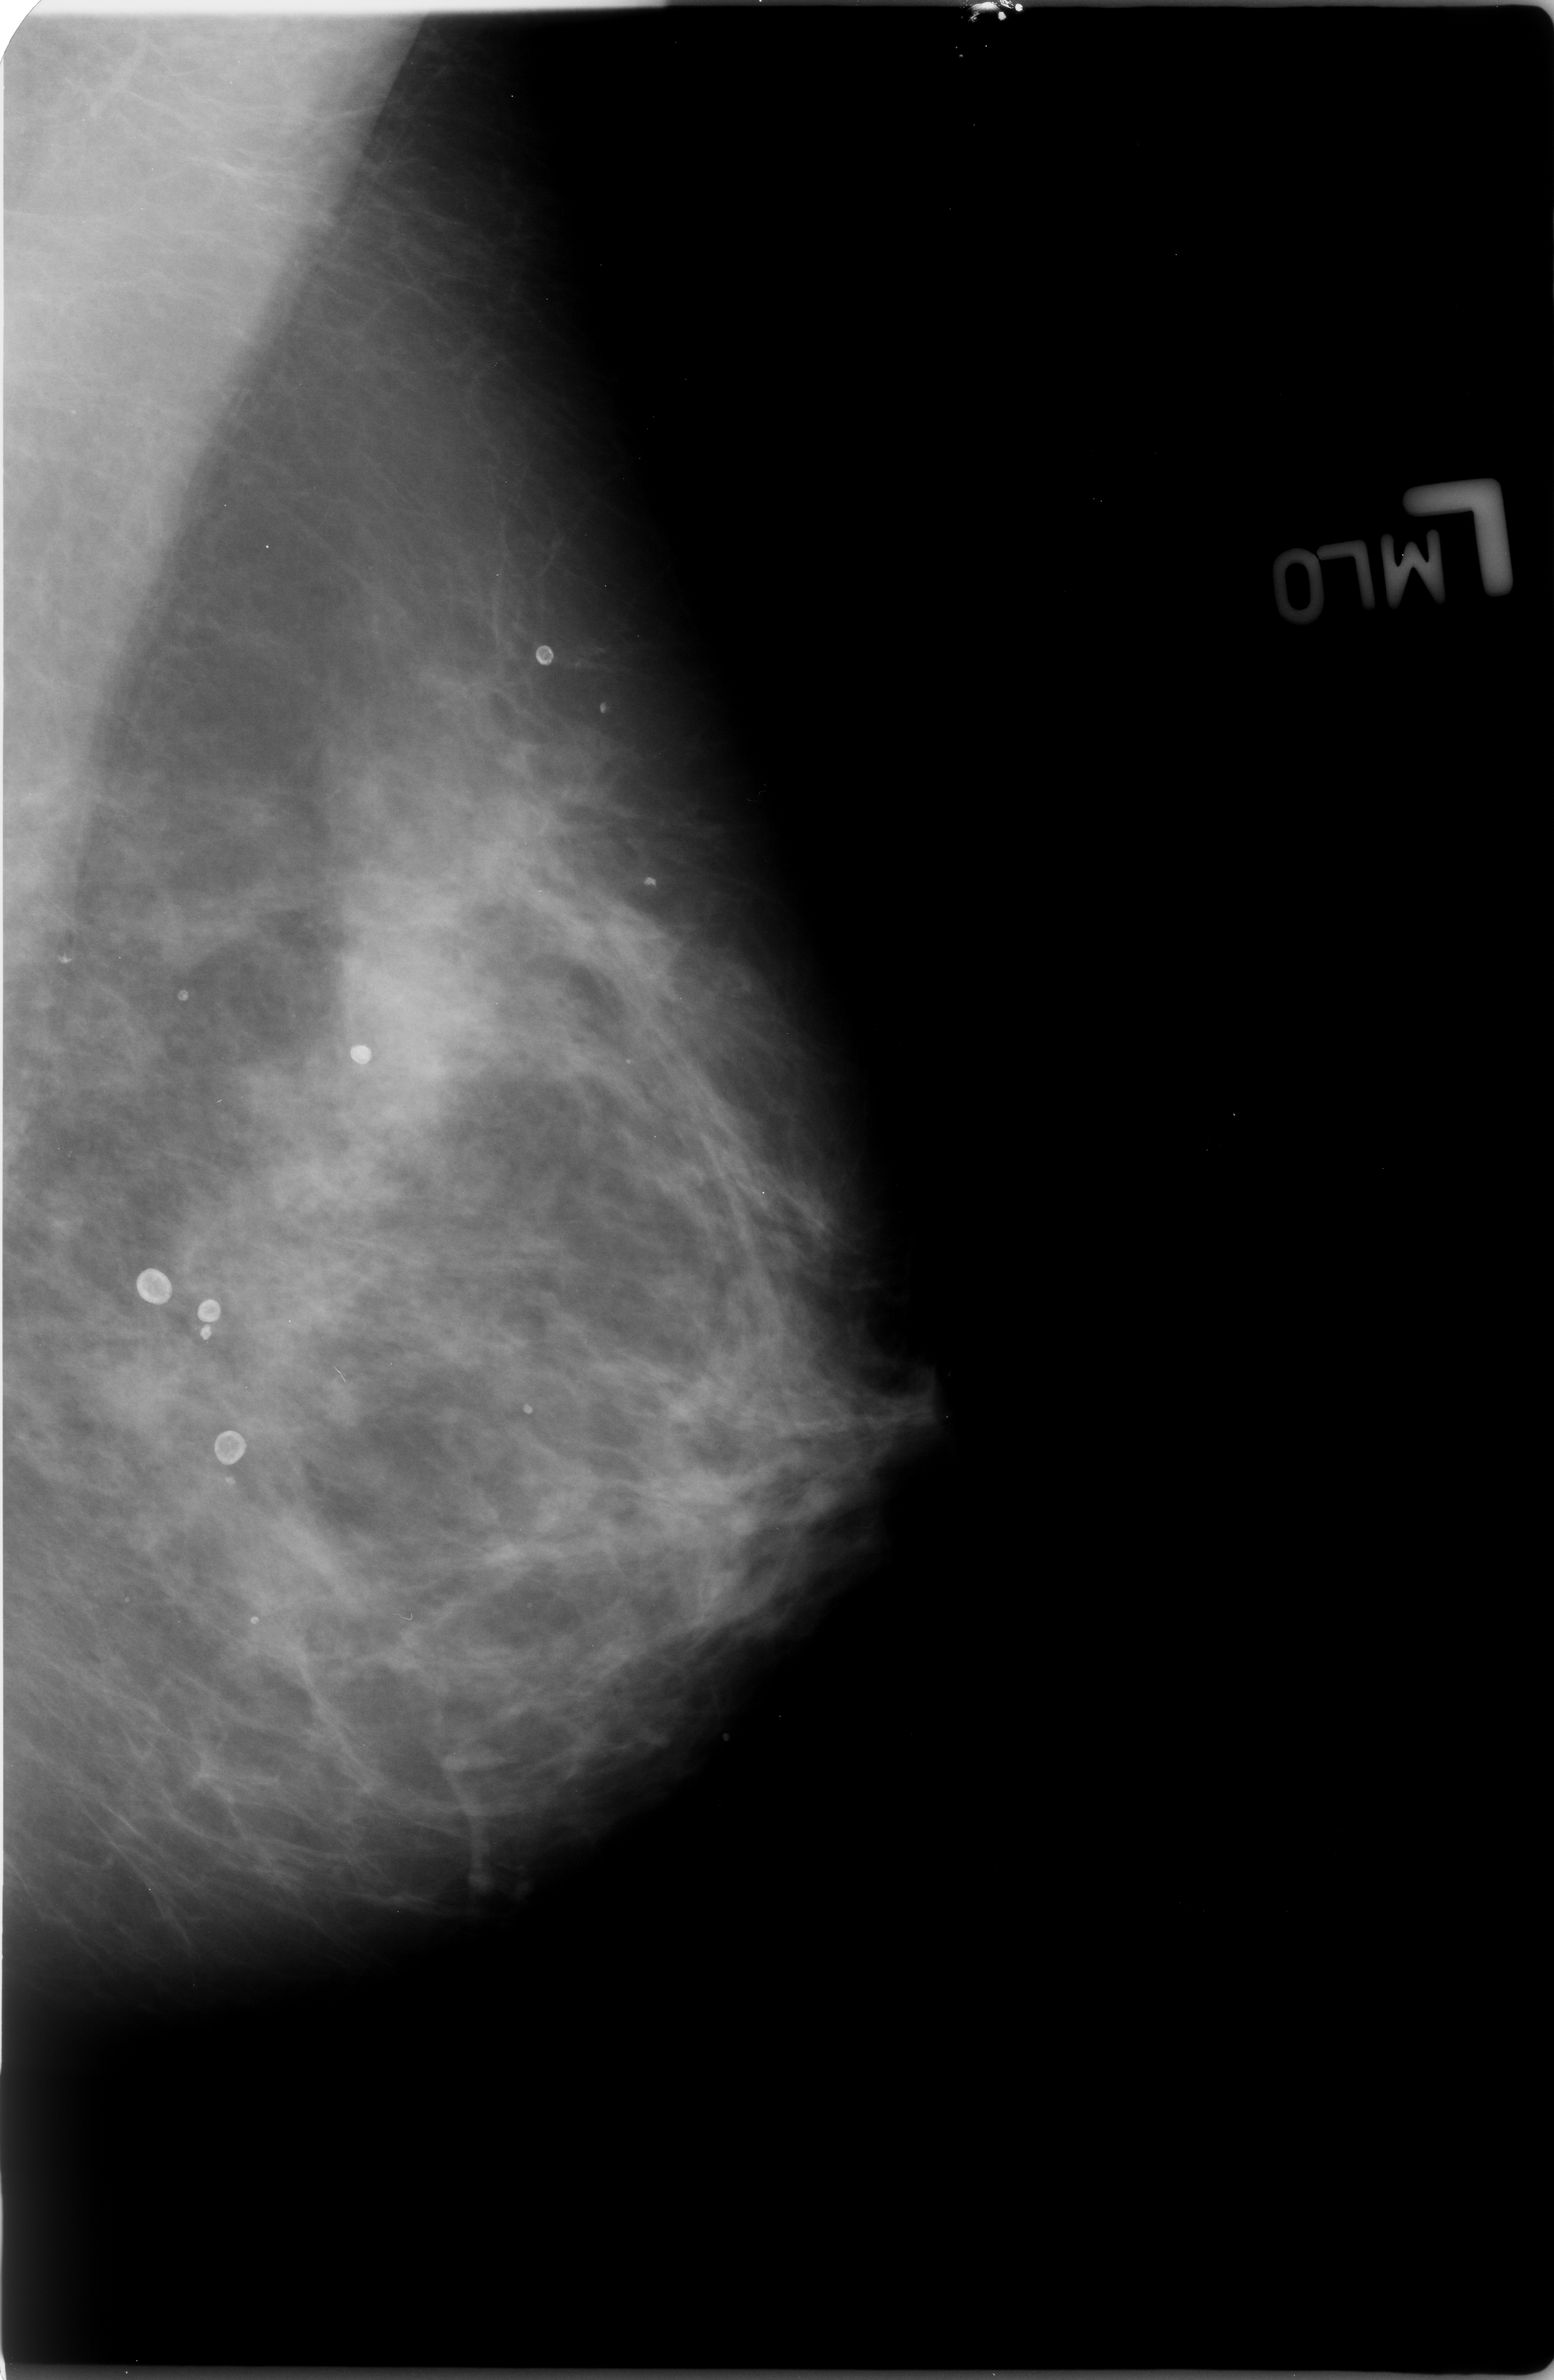
Mammogram (digitized film), left breast, mediolateral oblique (MLO) view, BI-RADS breast density category 3 (scale 1–4).
Abnormality record for this image: Finding 1 of 6: calcifications, morphology round and regular / eggshell; BI-RADS assessment category 2; benign without callback (not worked up further). Finding 2 of 6: calcifications, morphology round and regular / eggshell; BI-RADS assessment category 2; benign; no additional work-up was recommended (benign without callback). Finding 3 of 6: calcifications, morphology round and regular / eggshell; BI-RADS assessment category 2; benign; no additional work-up was recommended (benign without callback). Finding 4 of 6: calcifications, morphology round and regular / eggshell; BI-RADS assessment category 2; benign; no additional work-up was recommended (benign without callback). Finding 5 of 6: calcifications, morphology round and regular / eggshell; BI-RADS assessment category 2; subtlety rating 3 on a 1 (subtle) to 5 (obvious) scale; benign without callback (not worked up further). Finding 6 of 6: calcifications, morphology round and regular / eggshell; BI-RADS assessment category 2; subtlety rating 3 on a 1 (subtle) to 5 (obvious) scale; benign without callback (not worked up further).